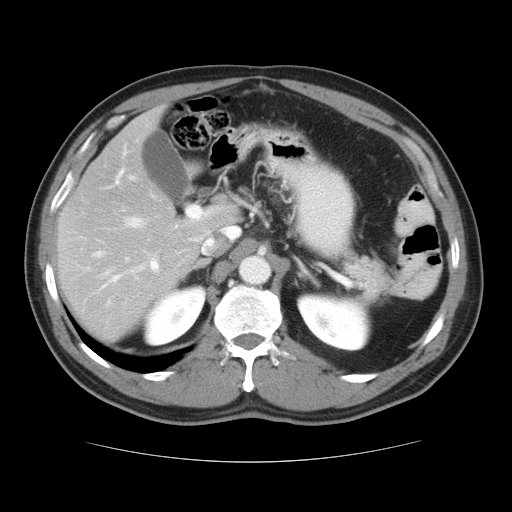
Contrast-enhanced abdominal CT, one axial slice. Position 22 of 37 along the scan axis. Reconstruction kernel STANDARD. 120 kVp. Intravenous contrast given. Soft-tissue window (W 400 / L 40 HU). 512 × 512 image matrix, field of view 374 × 374 mm. Male patient, age 66 years. Case-level facts recorded for this patient, not image findings: diagnosis: colorectal cancer liver metastases, imaged before liver resection; multiple liver metastases: yes; largest metastasis: 1.6 cm; disease in both lobes: yes.
Outlined on this slice (outlined manually by an expert reader):
- hepatic veins: bounding box <93,175,223,261> (left, top, right, bottom; pixels)
- liver: <58,108,240,341>
- planned liver remnant (the part of the liver to remain after resection): <58,202,240,341>
- portal vein (with intrahepatic branches): <102,145,213,288>